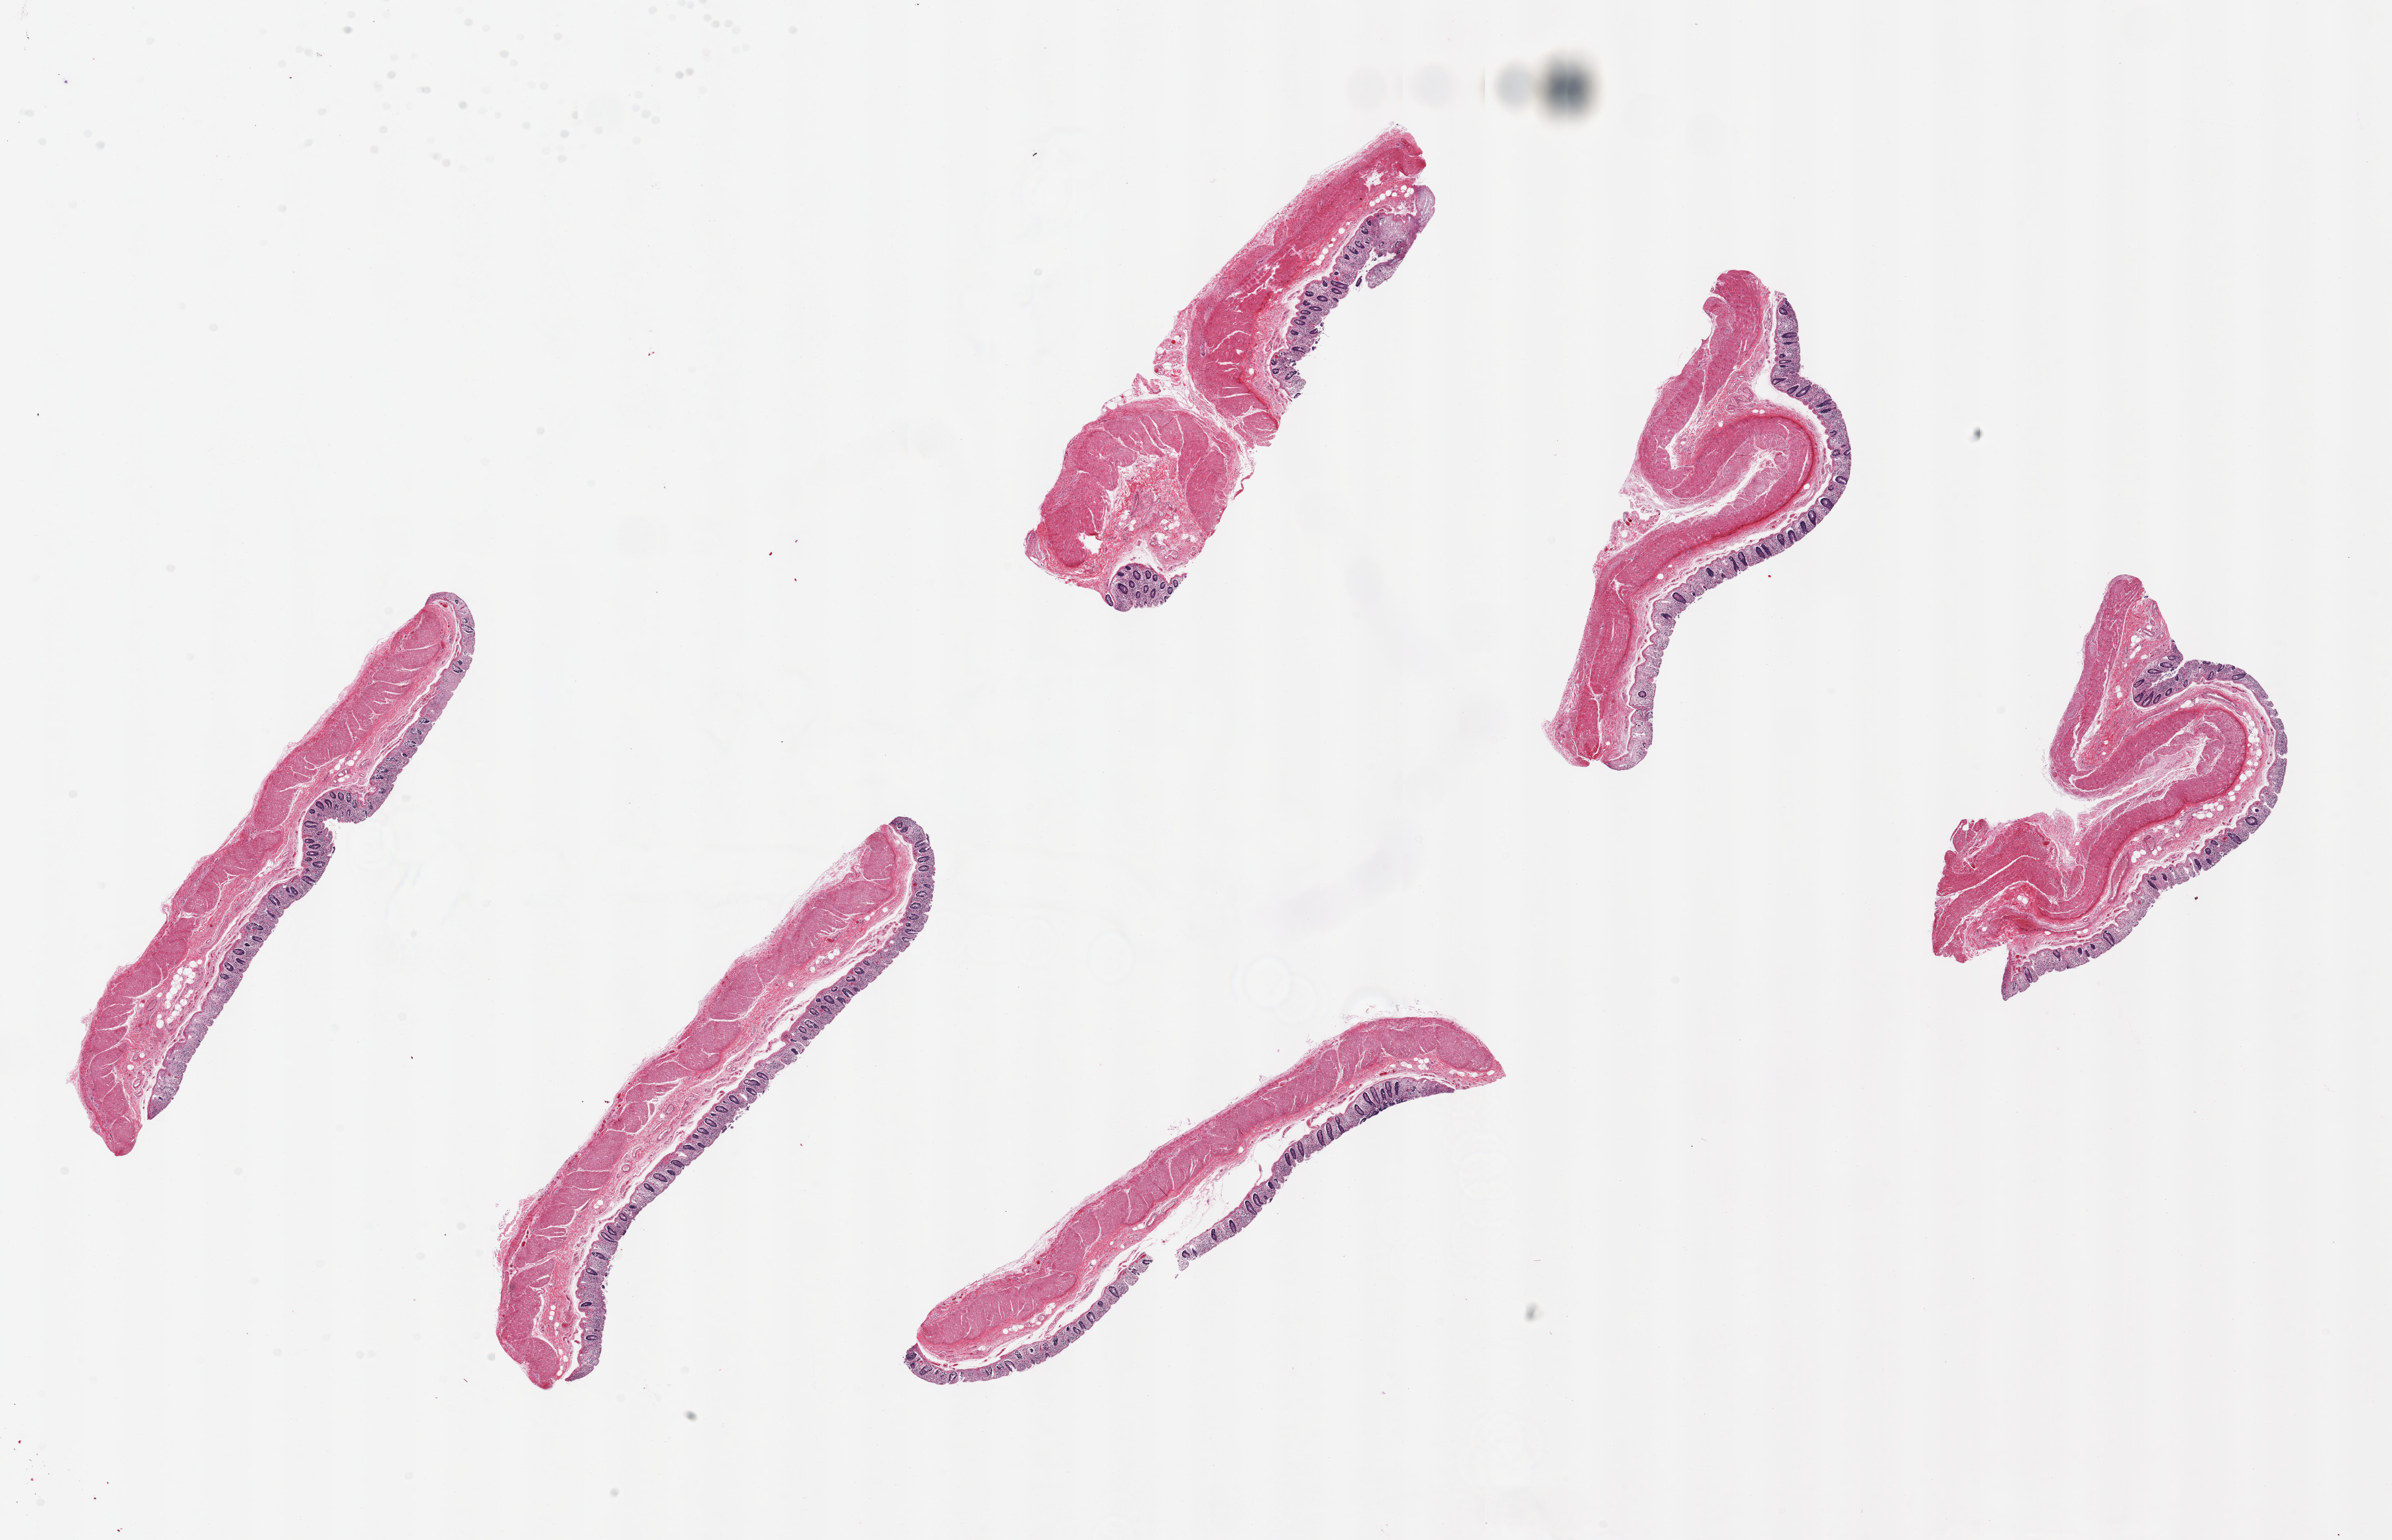
Hematoxylin and eosin (H&E) whole-slide image — a low-resolution overview of the entire scanned area, about 28.5 x 18.4 mm, PAXgene-fixed, paraffin-embedded tissue, sampled site (target tissue): transverse colon, donor tissue sample. Donor: male.
- reviewer comment on this tissue sample: 6 pieces ~7x1mm @0-30% badly autolzyed mucosa